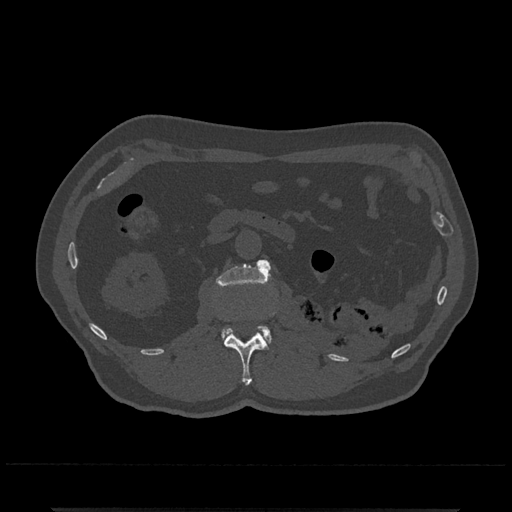
CT including the spine, one axial slice; position 333 of 797 along the scan axis; reconstruction kernel Br40s/3; 120 kVp; bone window (W 1800 / L 400 HU); 0.5 mm slice thickness; 512 × 512 image matrix, field of view 393 × 393 mm. Patient: male, 67 years. Case-level facts recorded for this patient, not image findings: primary cancer: prostate.
Outlined on this slice (semi-automatically segmented with operator editing):
- L1 vertebra: bounding box <224,332,269,385> (left, top, right, bottom; pixels)
- L2 vertebra: <216,260,272,344>